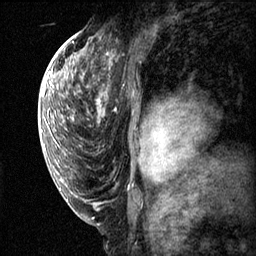
Breast MRI (dynamic contrast-enhanced), one sagittal slice. Position 38 of 60 along the scan axis. Dynamic contrast-enhanced series, image 2 of 3 at this slice position (ordered by acquisition). 1.5 T. TE 4.2 ms, TR 11.1 ms. 2 mm slice thickness. 256 × 256 image matrix, field of view 180 × 180 mm. Female patient, age 50 years.
Annotated regions visible in this slice (semi-automatically segmented with operator editing):
- analysis volume of interest (the breast-tissue region the enhancement analysis was run in; not a lesion): bounding box [x1, y1, x2, y2] px = [82, 56, 167, 143]
- tumour enhancement mask (voxels above the 70 % enhancement threshold inside the analysis volume of interest): [98, 92, 158, 139]